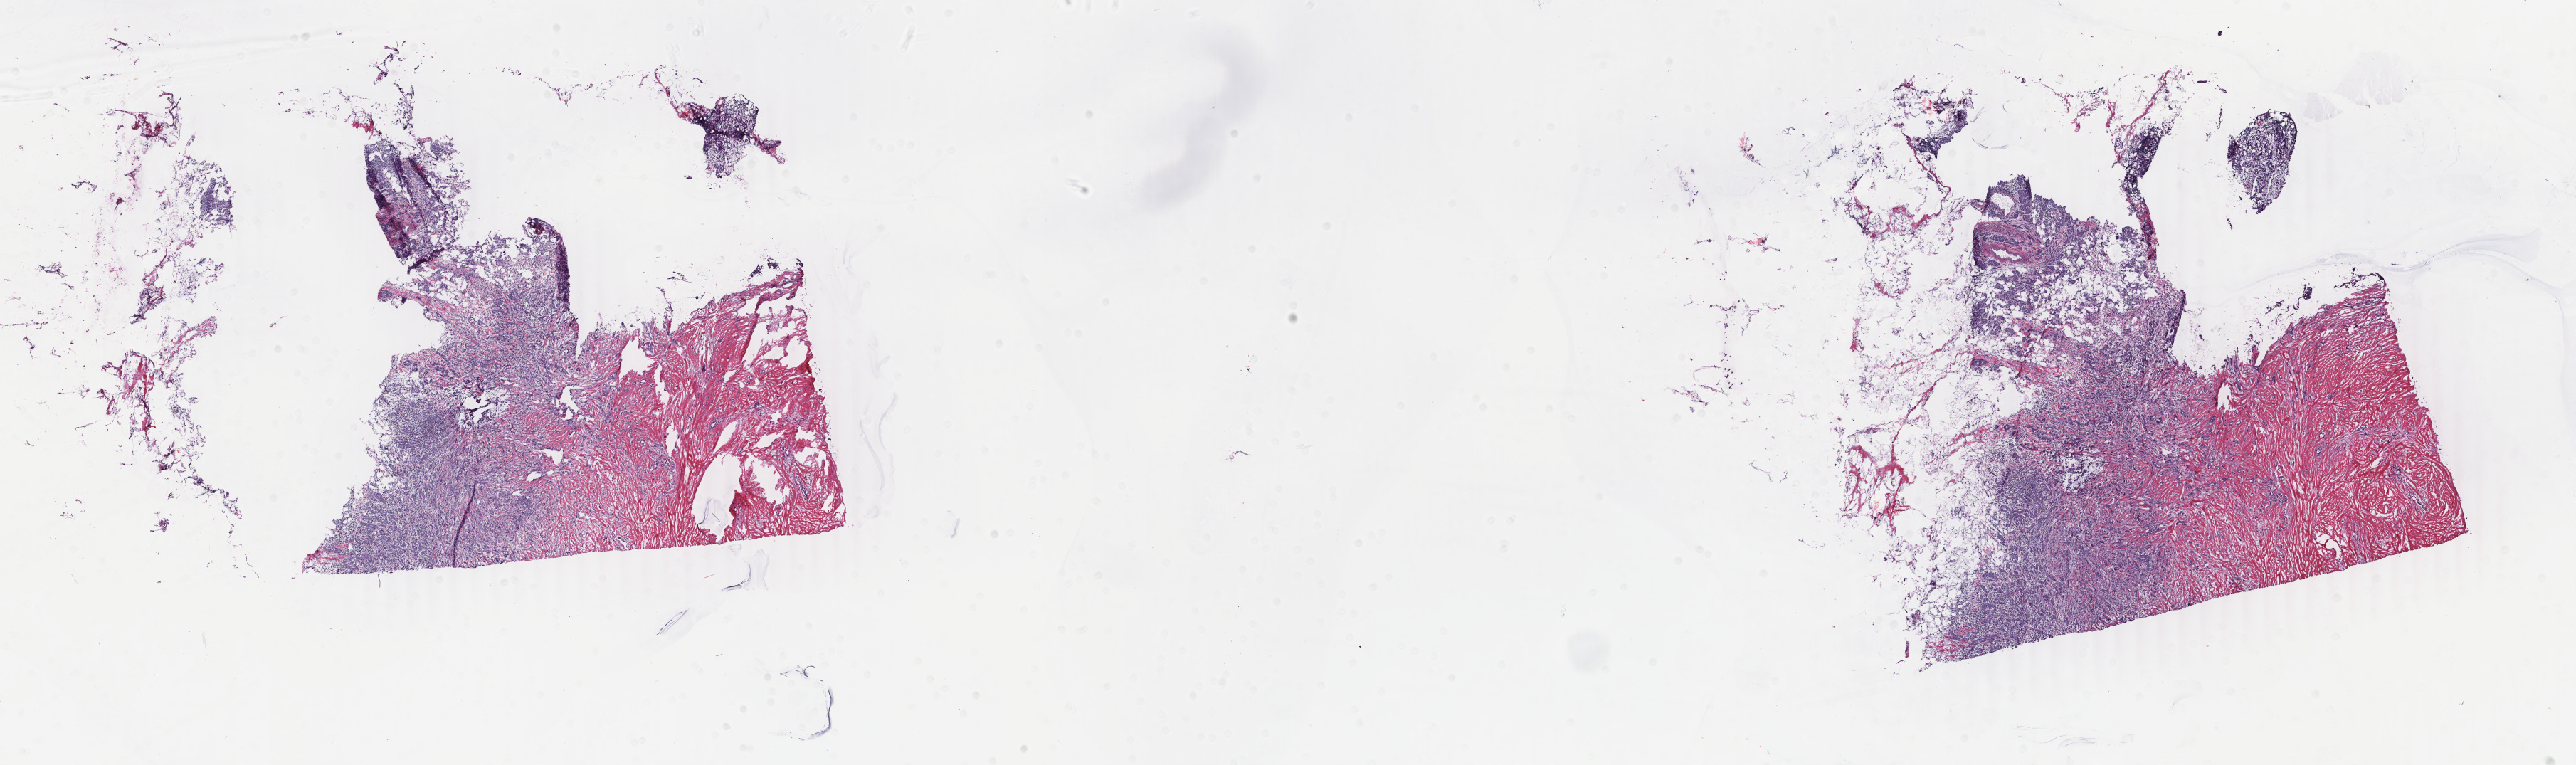
H&E whole-slide image, shown as a low-resolution overview of the whole scanned area (about 28.8 x 8.6 mm, slide scanned at 40x), frozen section from the bottom of the tissue portion, sample: primary tumour, breast. Female patient; age at initial diagnosis 40 years. Composition of this section per pathologist review: tumour cells 60%, tumour nuclei 60%, normal cells 0%, stromal cells 40%, necrosis 0%. Inflammatory infiltration, as recorded: lymphocyte infiltration 50%, monocyte infiltration 20%, neutrophil infiltration 20%.
• pathologic diagnosis: Infiltrating duct carcinoma, NOS
• laterality: right